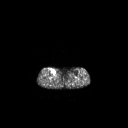
FDG PET of an extremity soft-tissue mass (from a PET/CT study), one axial slice; slice 134 of 267 in the series (ordered by position); 3.27 mm slice thickness; 128 × 128 image matrix, field of view 700 × 700 mm. Female patient, age 65 years. Case-level facts recorded for this patient, not image findings: histological type: undifferentiated – high grade; grade: high; site of the primary tumour: right thigh.
Structures marked on this image (expert contour drawn on MRI and transferred to this co-registered scan by the dataset authors):
- gross tumour volume (mass): bounding box (x1, y1, x2, y2) in pixels: (51, 69, 56, 74)